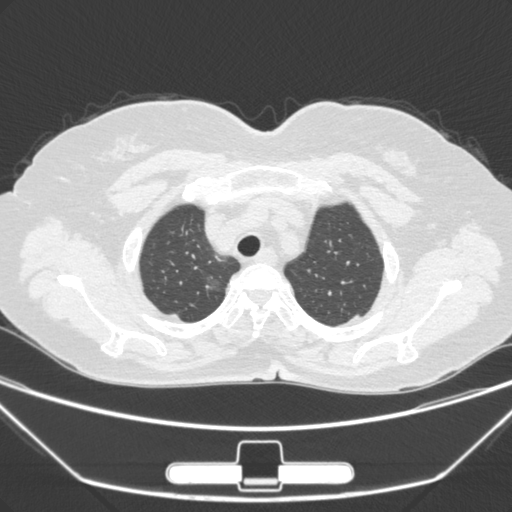
Chest CT, one axial slice. Position 235 of 275 along the scan axis. 120 kVp. Lung window (W 1500 / L -600 HU). 1 mm slice thickness. 512 × 512 image matrix. Female patient, age 63 years. Case-level facts recorded for this patient, not image findings: clinical TNM (as recorded): T1a N0 M0.
Annotated regions visible in this slice (bounding box drawn by a radiologist):
- lung tumour (recorded histology: adenocarcinoma): bounding box <194,269,226,299> (left, top, right, bottom; pixels)